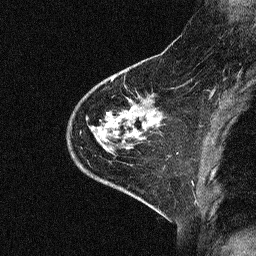
Breast MRI (dynamic contrast-enhanced), one sagittal slice. Slice 17 of 64 in the series (ordered by position). Dynamic contrast-enhanced study with each time point stored as its own series, time point 2 of 3 at this slice position (early post-contrast, ordered by acquisition time). 1.5 T. TE 4.5 ms, TR 11 ms. 256 × 256 image matrix, field of view 200 × 200 mm. Female patient, age 46 years. Case-level facts recorded for this patient, not image findings: setting: breast cancer imaged before/during neoadjuvant chemotherapy; receptor status: HER2-positive.
Outlined on this slice (semi-automatic segmentation, software-assisted and operator-edited):
- analysis volume of interest (the breast-tissue region the enhancement analysis was run in; not a lesion): bounding box (x1, y1, x2, y2) in pixels: (46, 51, 180, 169)
- tumour enhancement mask (voxels above the 90 % enhancement threshold inside the analysis volume of interest): (104, 121, 108, 141)